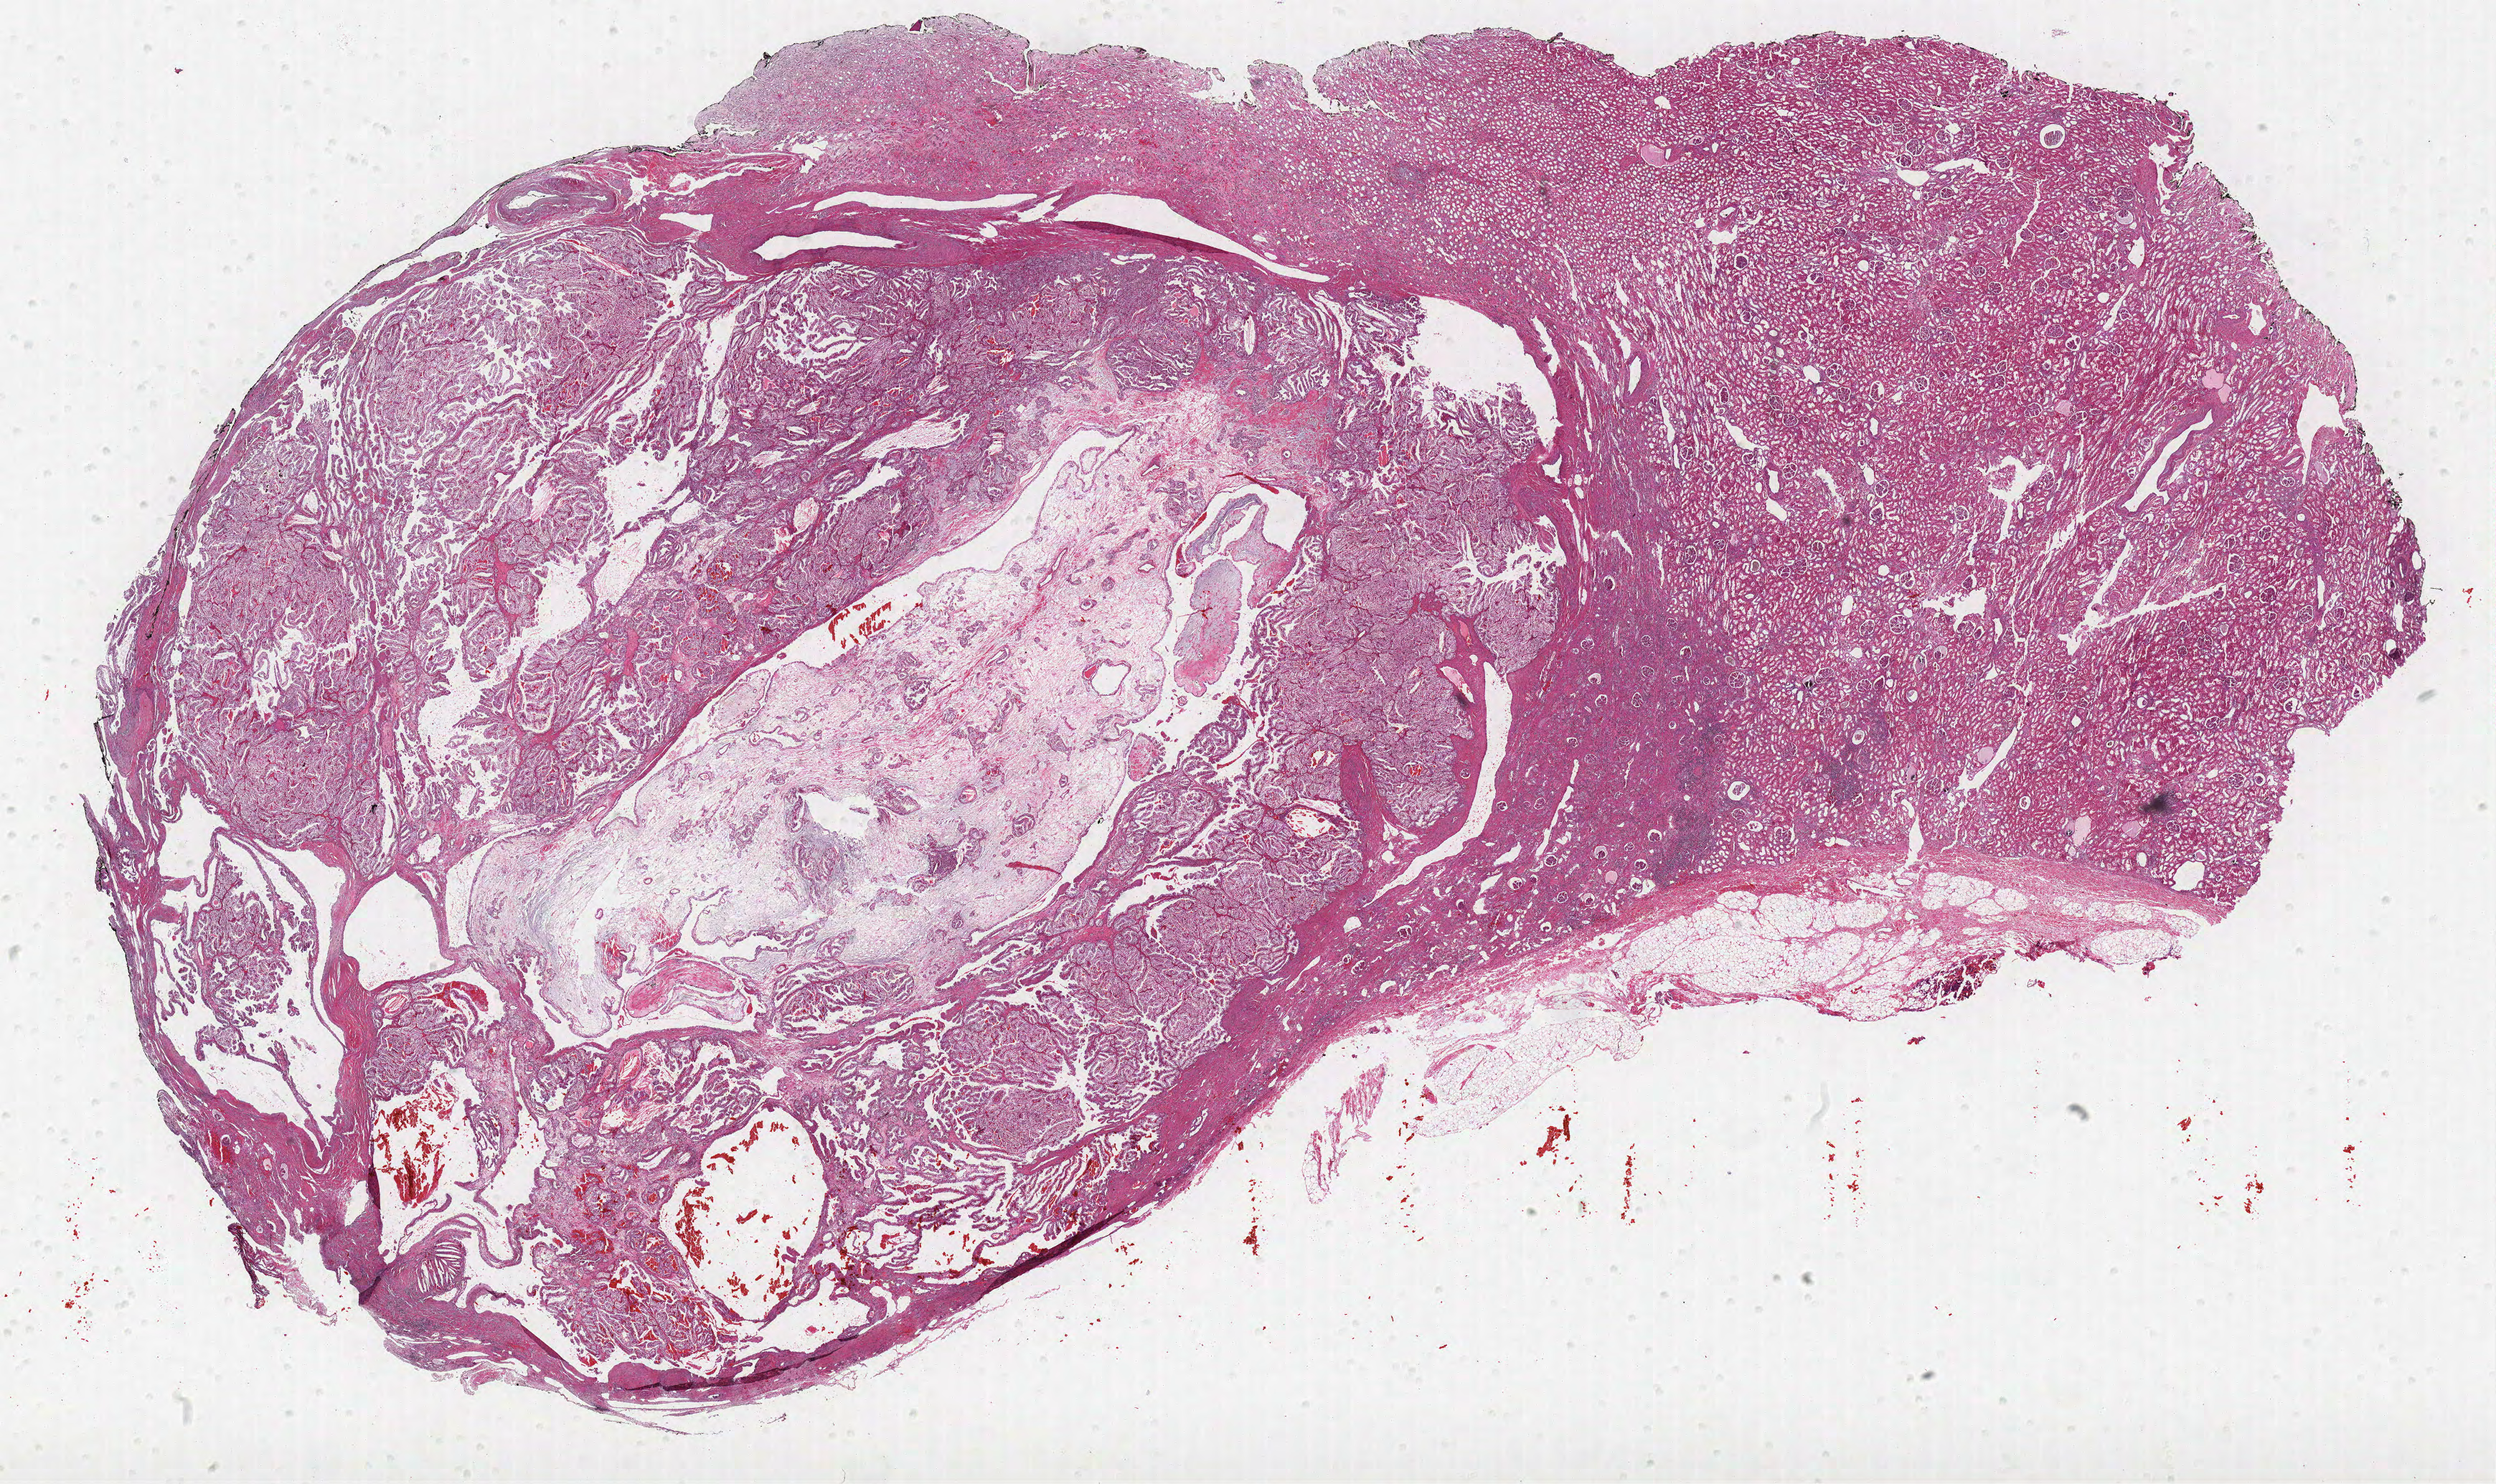
H&E whole-slide image — shown as a low-resolution overview of the whole scanned area (about 27.8 x 16.5 mm, slide scanned at 40x). FFPE section. Kidney, primary tumour sample. Male patient; age at initial diagnosis 69 years. Histologic grade: G2 (moderately differentiated).
- AJCC pathologic stage: I
- histologic diagnosis: Clear cell adenocarcinoma, NOS